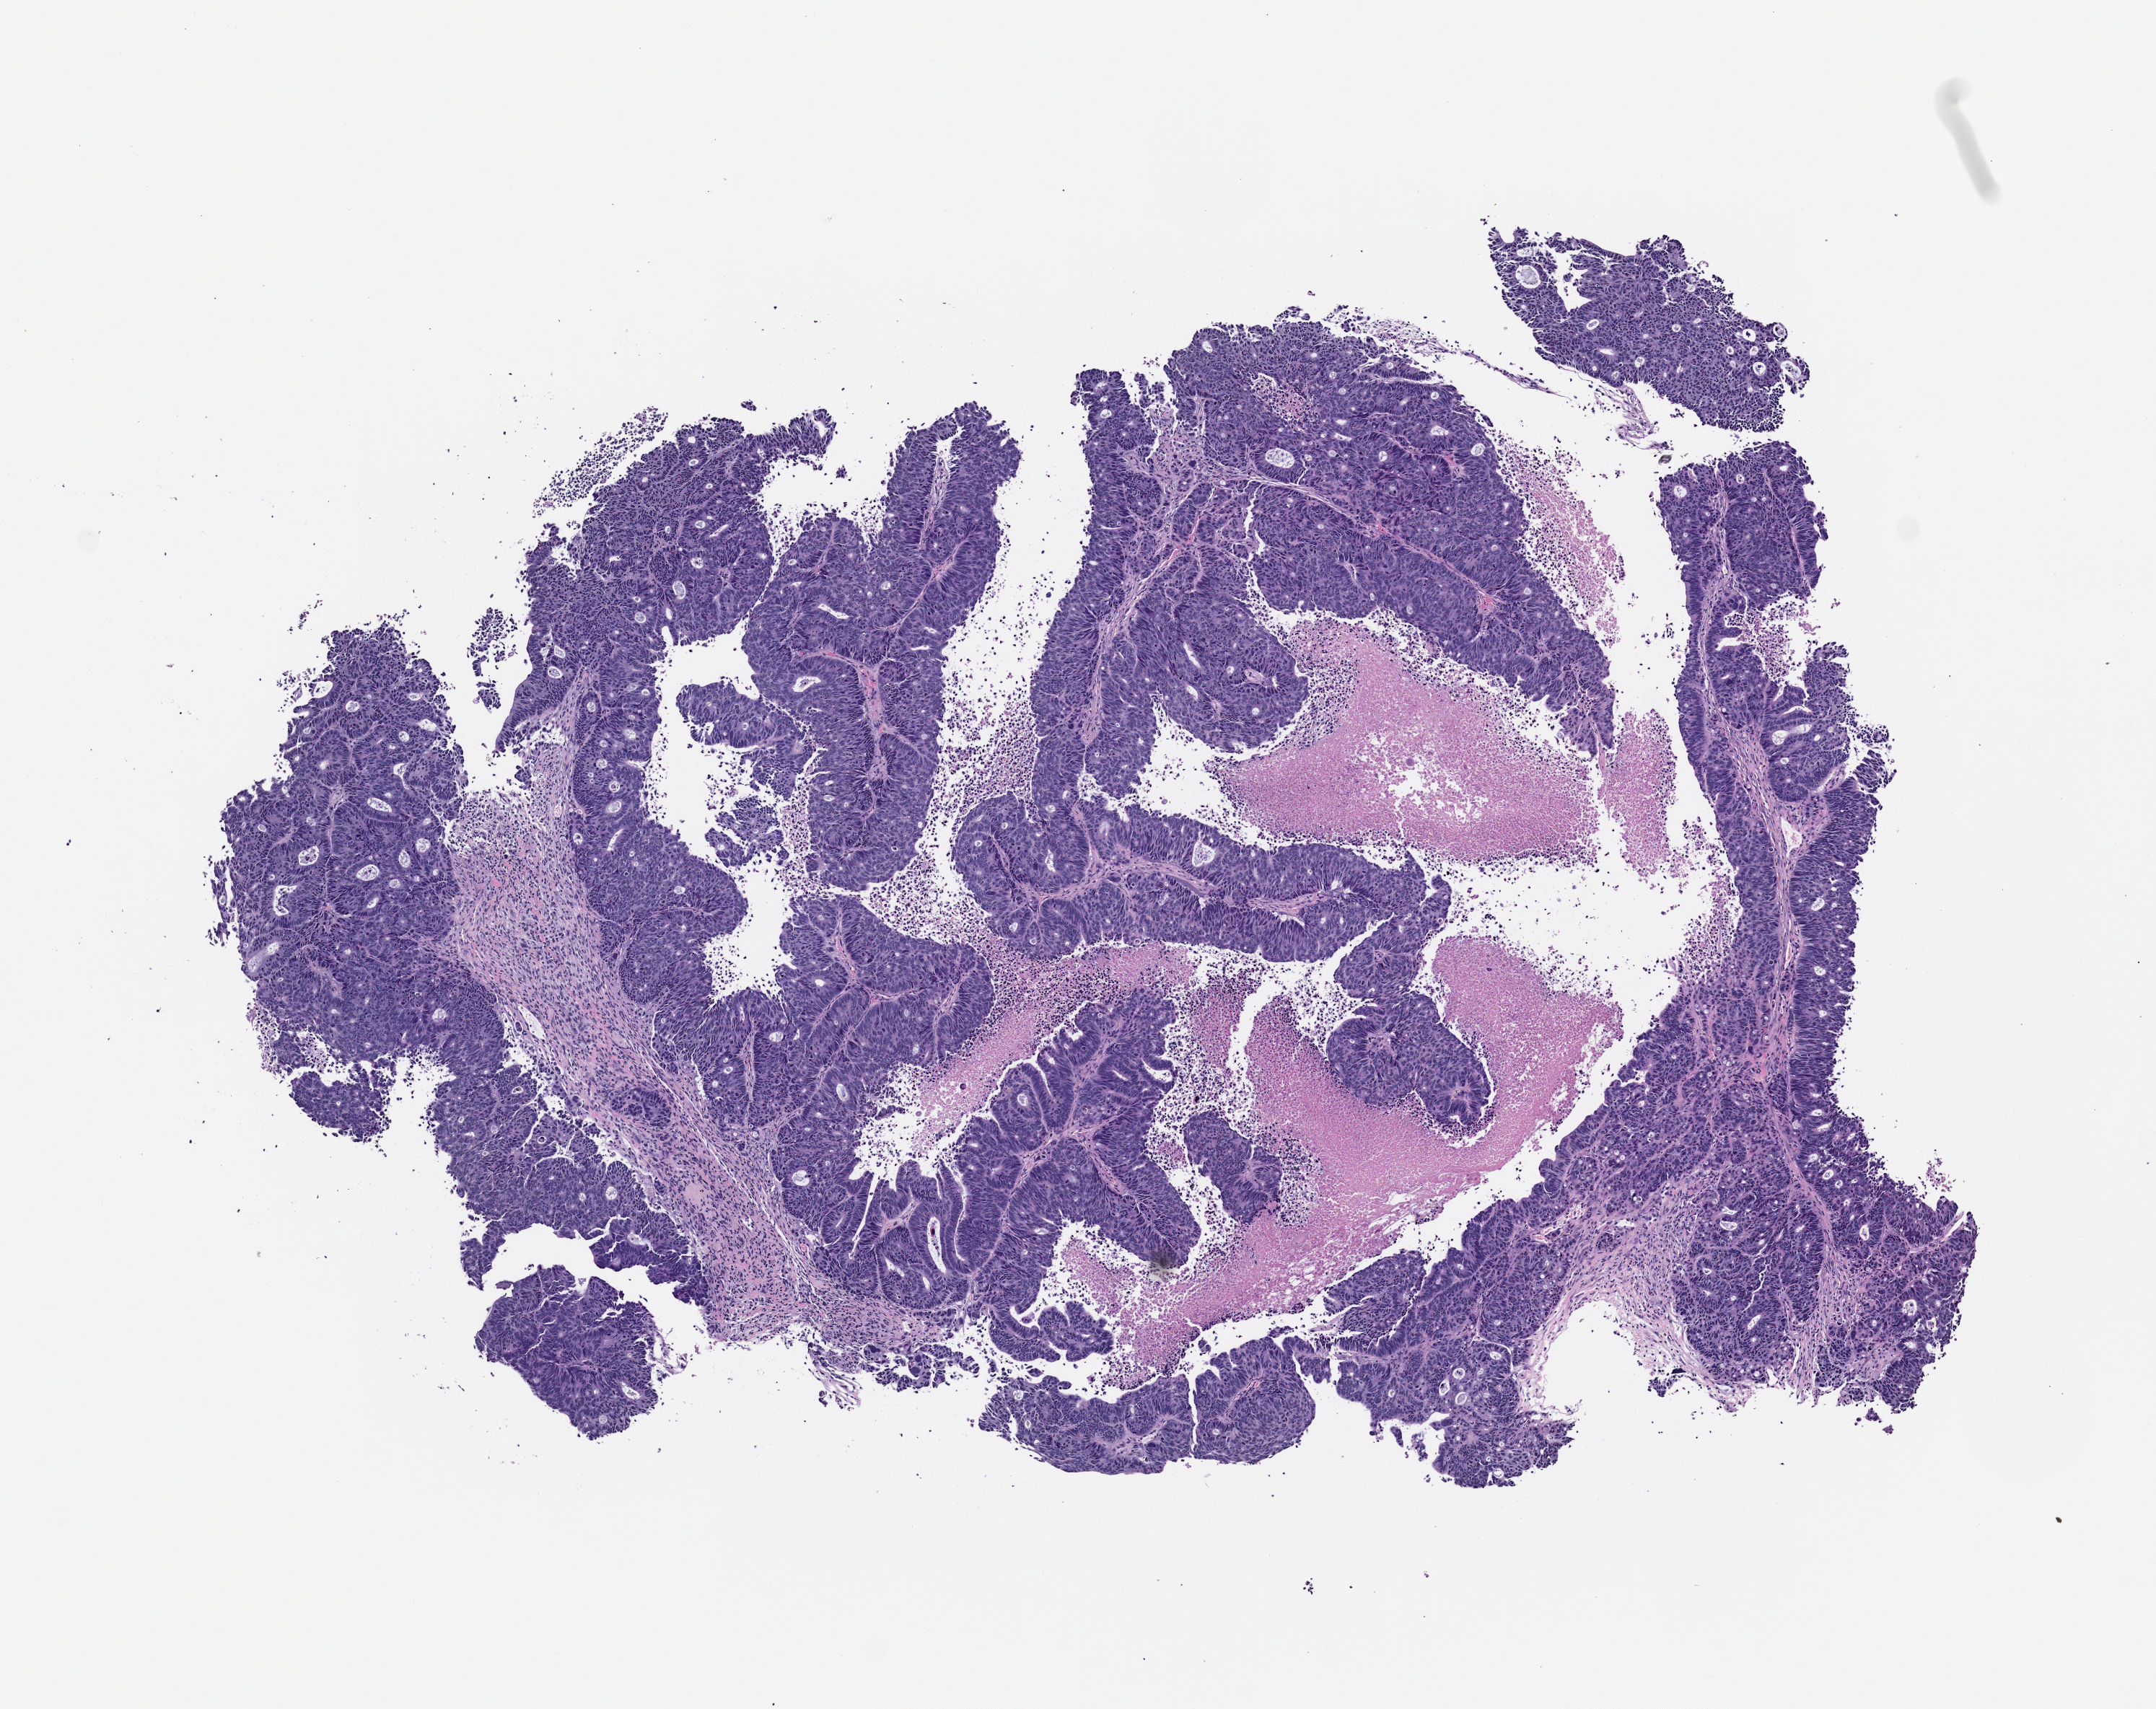
Whole-slide image, haematoxylin and eosin: patient-derived xenograft (human tumor grown in a mouse), passage 2, whole scanned area (about 6.0 x 4.8 mm) shown as a low-resolution overview. FFPE section. Tumor site category: colon.
Originating patient diagnosis: Colon Adenocarcinoma.